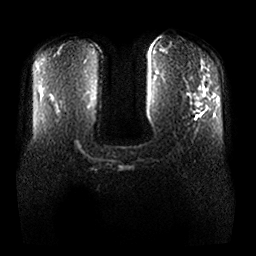
Breast MRI, one axial slice; diffusion-weighted series; image 2 of 4 stored at this slice position (different b-values; order by instance number); 1.5 T; 4 mm slice thickness; 256 × 256 image matrix, field of view 370 × 370 mm. Female patient.
Structures marked on this image (outlined manually by an expert reader):
- tumour on diffusion-weighted imaging: bounding box [x1, y1, x2, y2] px = [196, 97, 200, 106]